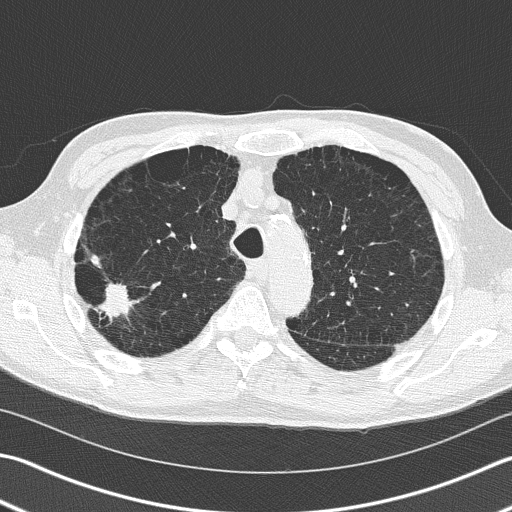
Axial slice from a low-dose chest CT screening exam, baseline annual screen, lung window (W 1500 / L -600 HU), 2 mm slice thickness, lung (sharp) reconstruction kernel (B50f), slice 46 of 163 in the series. Male, age 66 years at enrolment. Current smoker at enrolment.
Expert-annotated lung lesion, bounding box <74,256,141,339> (left, top, right, bottom; pixels). Reader record for this screening exam (exam-level; its link to the box is not recorded): non-calcified nodule or mass ≥4 mm, right upper lobe, 39 × 23 mm, spiculated (stellate) margins, soft tissue attenuation. Official screen result: positive, change unspecified: nodule(s) >= 4 mm or enlarging nodule(s), mass(es), or other non-specific abnormalities suspicious for lung cancer. Lung cancer was diagnosed 36 days after this screen: squamous cell carcinoma, NOS, right upper lobe, poorly differentiated (G3), stage IB (AJCC 6th edition), 23 mm at pathology.